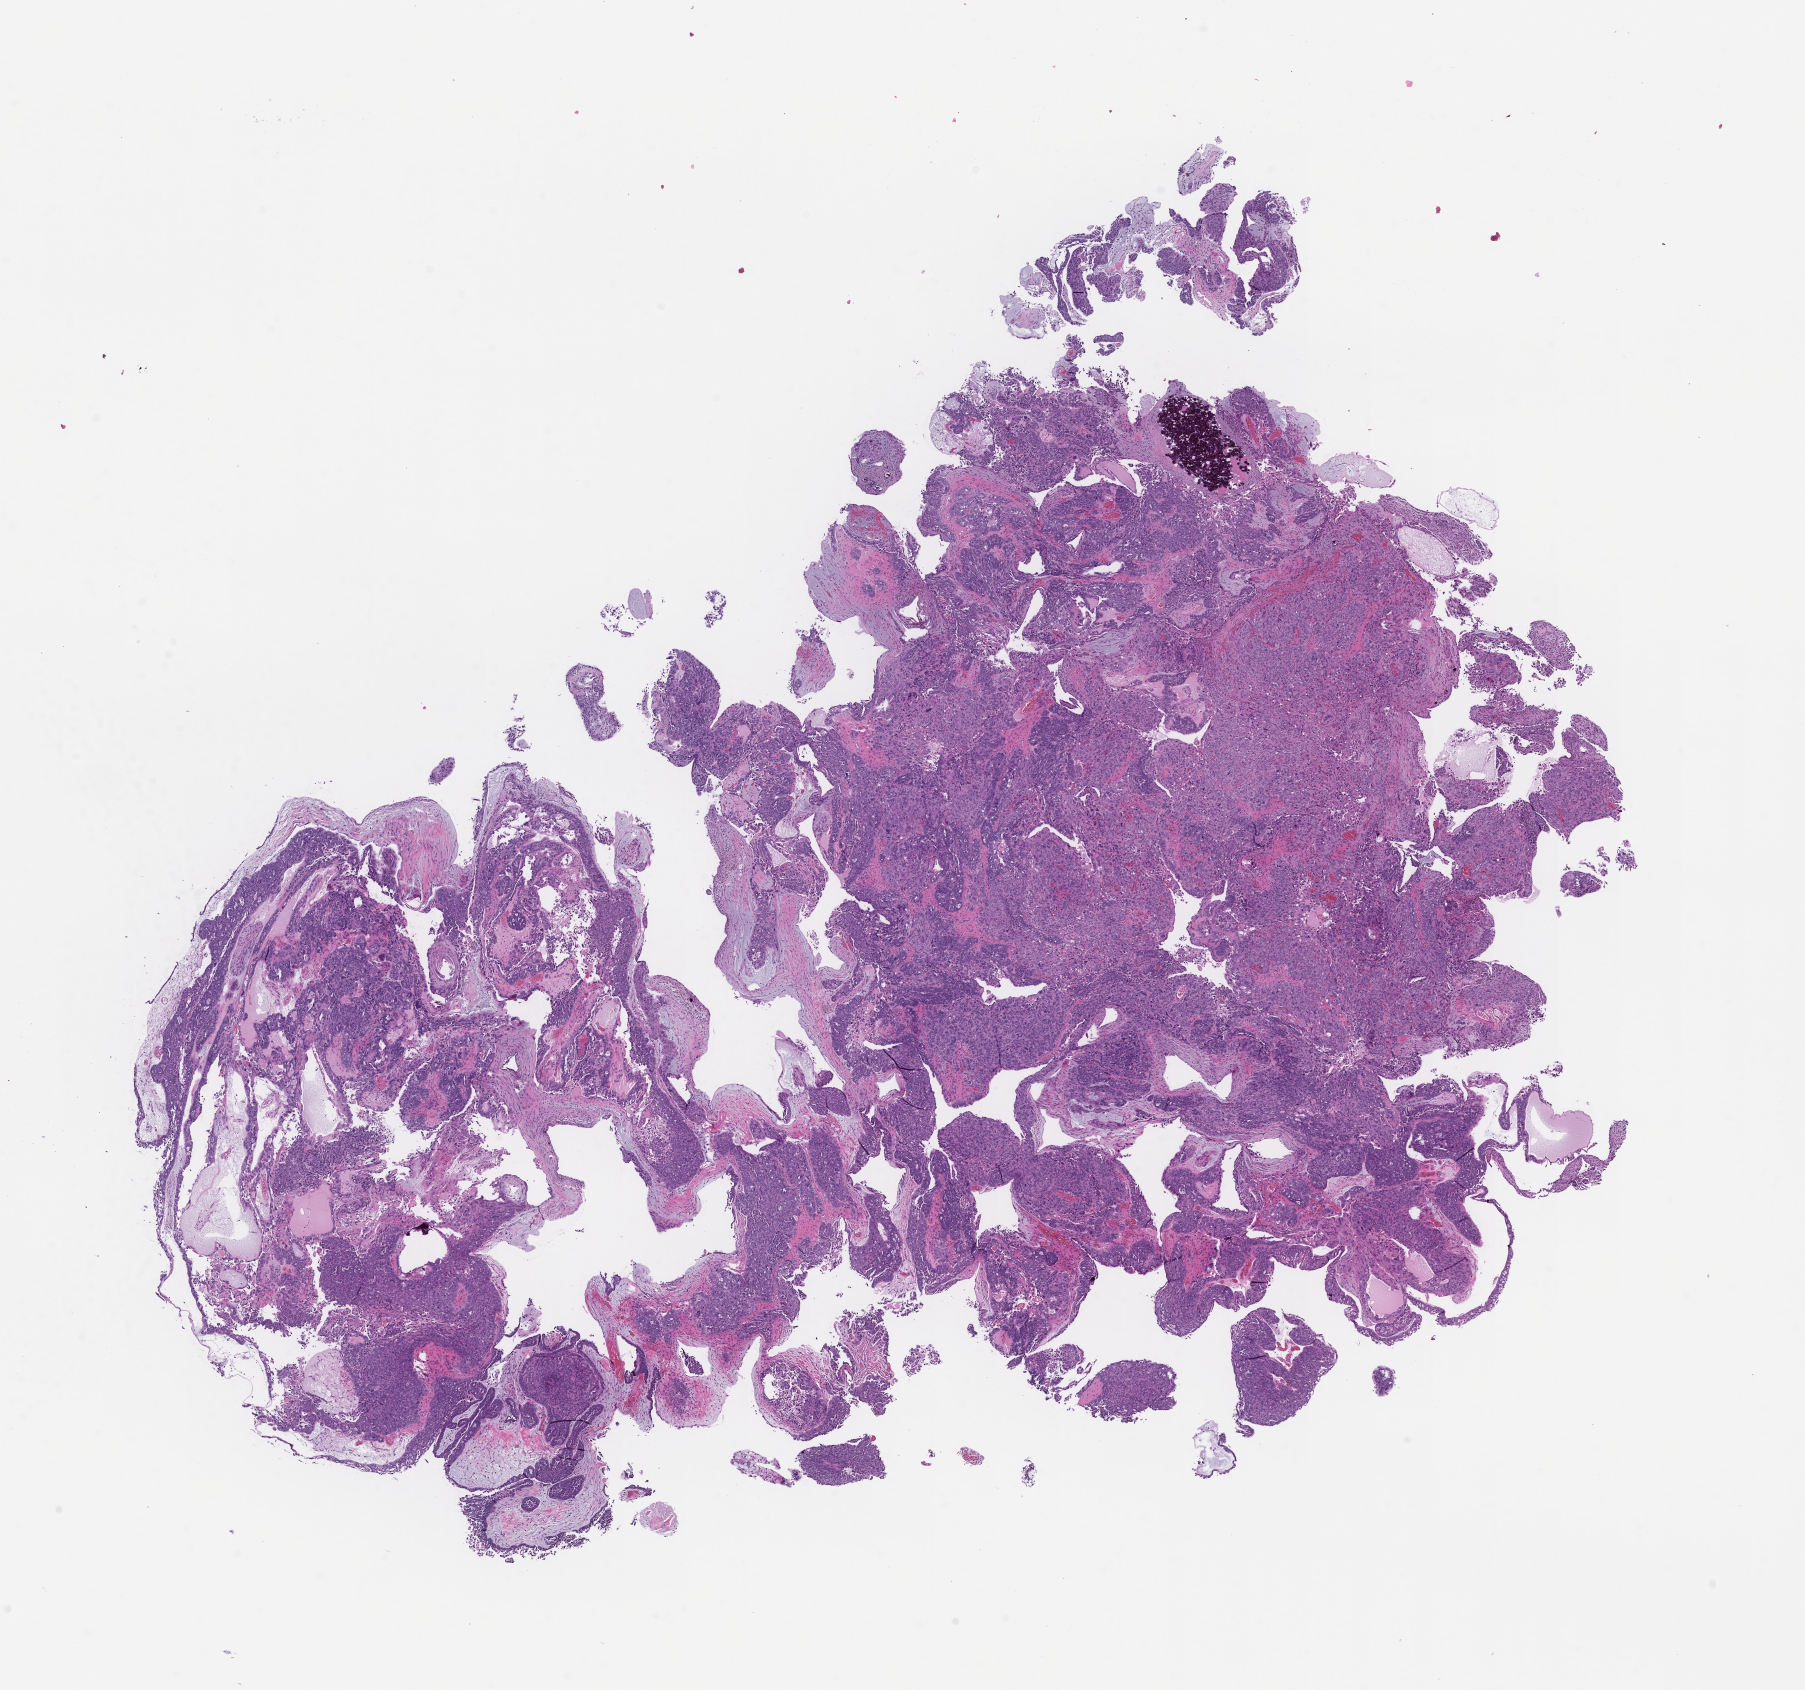
Digitized hematoxylin and eosin (H&E)-stained section — low-resolution overview of the scanned area, about 14.6 x 13.6 mm. Formalin-fixed, paraffin-embedded (FFPE) tissue. Tissue site: ovary. Specimen time point: collected at baseline (before treatment). Female patient.
This section: primary tumor. Diagnosis: Ovarian Carcinoma.